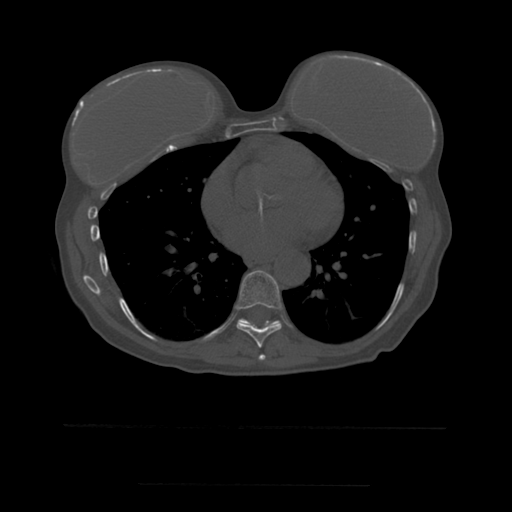
CT including the spine, one axial slice; position 335 of 544 along the scan axis; bone window (W 1800 / L 400 HU); 512 × 512 image matrix. Patient age 58 years. From the clinical record (not read from this slice): primary cancer: lung.
Outlined on this slice (semi-automatically segmented with operator editing):
- T7 vertebra: bounding box (x1, y1, x2, y2) in pixels: (259, 355, 266, 361)
- T8 vertebra: (236, 271, 282, 348)
- T9 vertebra: (238, 319, 279, 325)